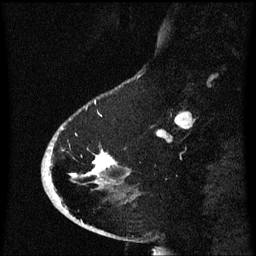
Breast MRI (dynamic contrast-enhanced), one sagittal slice; position 16 of 60 along the scan axis; dynamic contrast-enhanced series, image 2 of 3 at this slice position (ordered by acquisition); 1.5 T; TE 4.2 ms, TR 8.4 ms; 2.1 mm slice thickness; 256 × 256 image matrix. Patient: female, 53 years. Case-level facts recorded for this patient, not image findings: setting: breast cancer imaged before/during neoadjuvant chemotherapy; receptor status: HR-positive, HER2-negative.
Structures marked on this image (semi-automatic segmentation, software-assisted and operator-edited):
- analysis volume of interest (the breast-tissue region the enhancement analysis was run in; not a lesion): bounding box (x1, y1, x2, y2) in pixels: (49, 120, 130, 201)
- tumour enhancement mask (voxels above the 70 % enhancement threshold inside the analysis volume of interest): (76, 154, 116, 177)